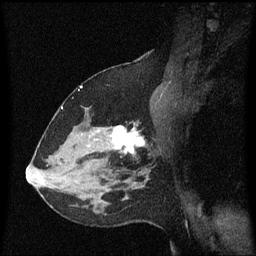
Breast MRI (dynamic contrast-enhanced), one sagittal slice. Dynamic contrast-enhanced series, image 2 of 3 at this slice position (ordered by acquisition). 1.5 T. TE 4.2 ms, TR 8.4 ms. 2 mm slice thickness. 256 × 256 image matrix, field of view 200 × 200 mm. Female patient, age 37 years. From the clinical record (not read from this slice): setting: breast cancer imaged before/during neoadjuvant chemotherapy; receptor status: HR-positive, HER2-negative.
Outlined on this slice (semi-automatic segmentation, software-assisted and operator-edited):
- analysis volume of interest (the breast-tissue region the enhancement analysis was run in; not a lesion): bounding box <95,110,155,171> (left, top, right, bottom; pixels)
- tumour enhancement mask (voxels above the 70 % enhancement threshold inside the analysis volume of interest): <113,126,145,155>